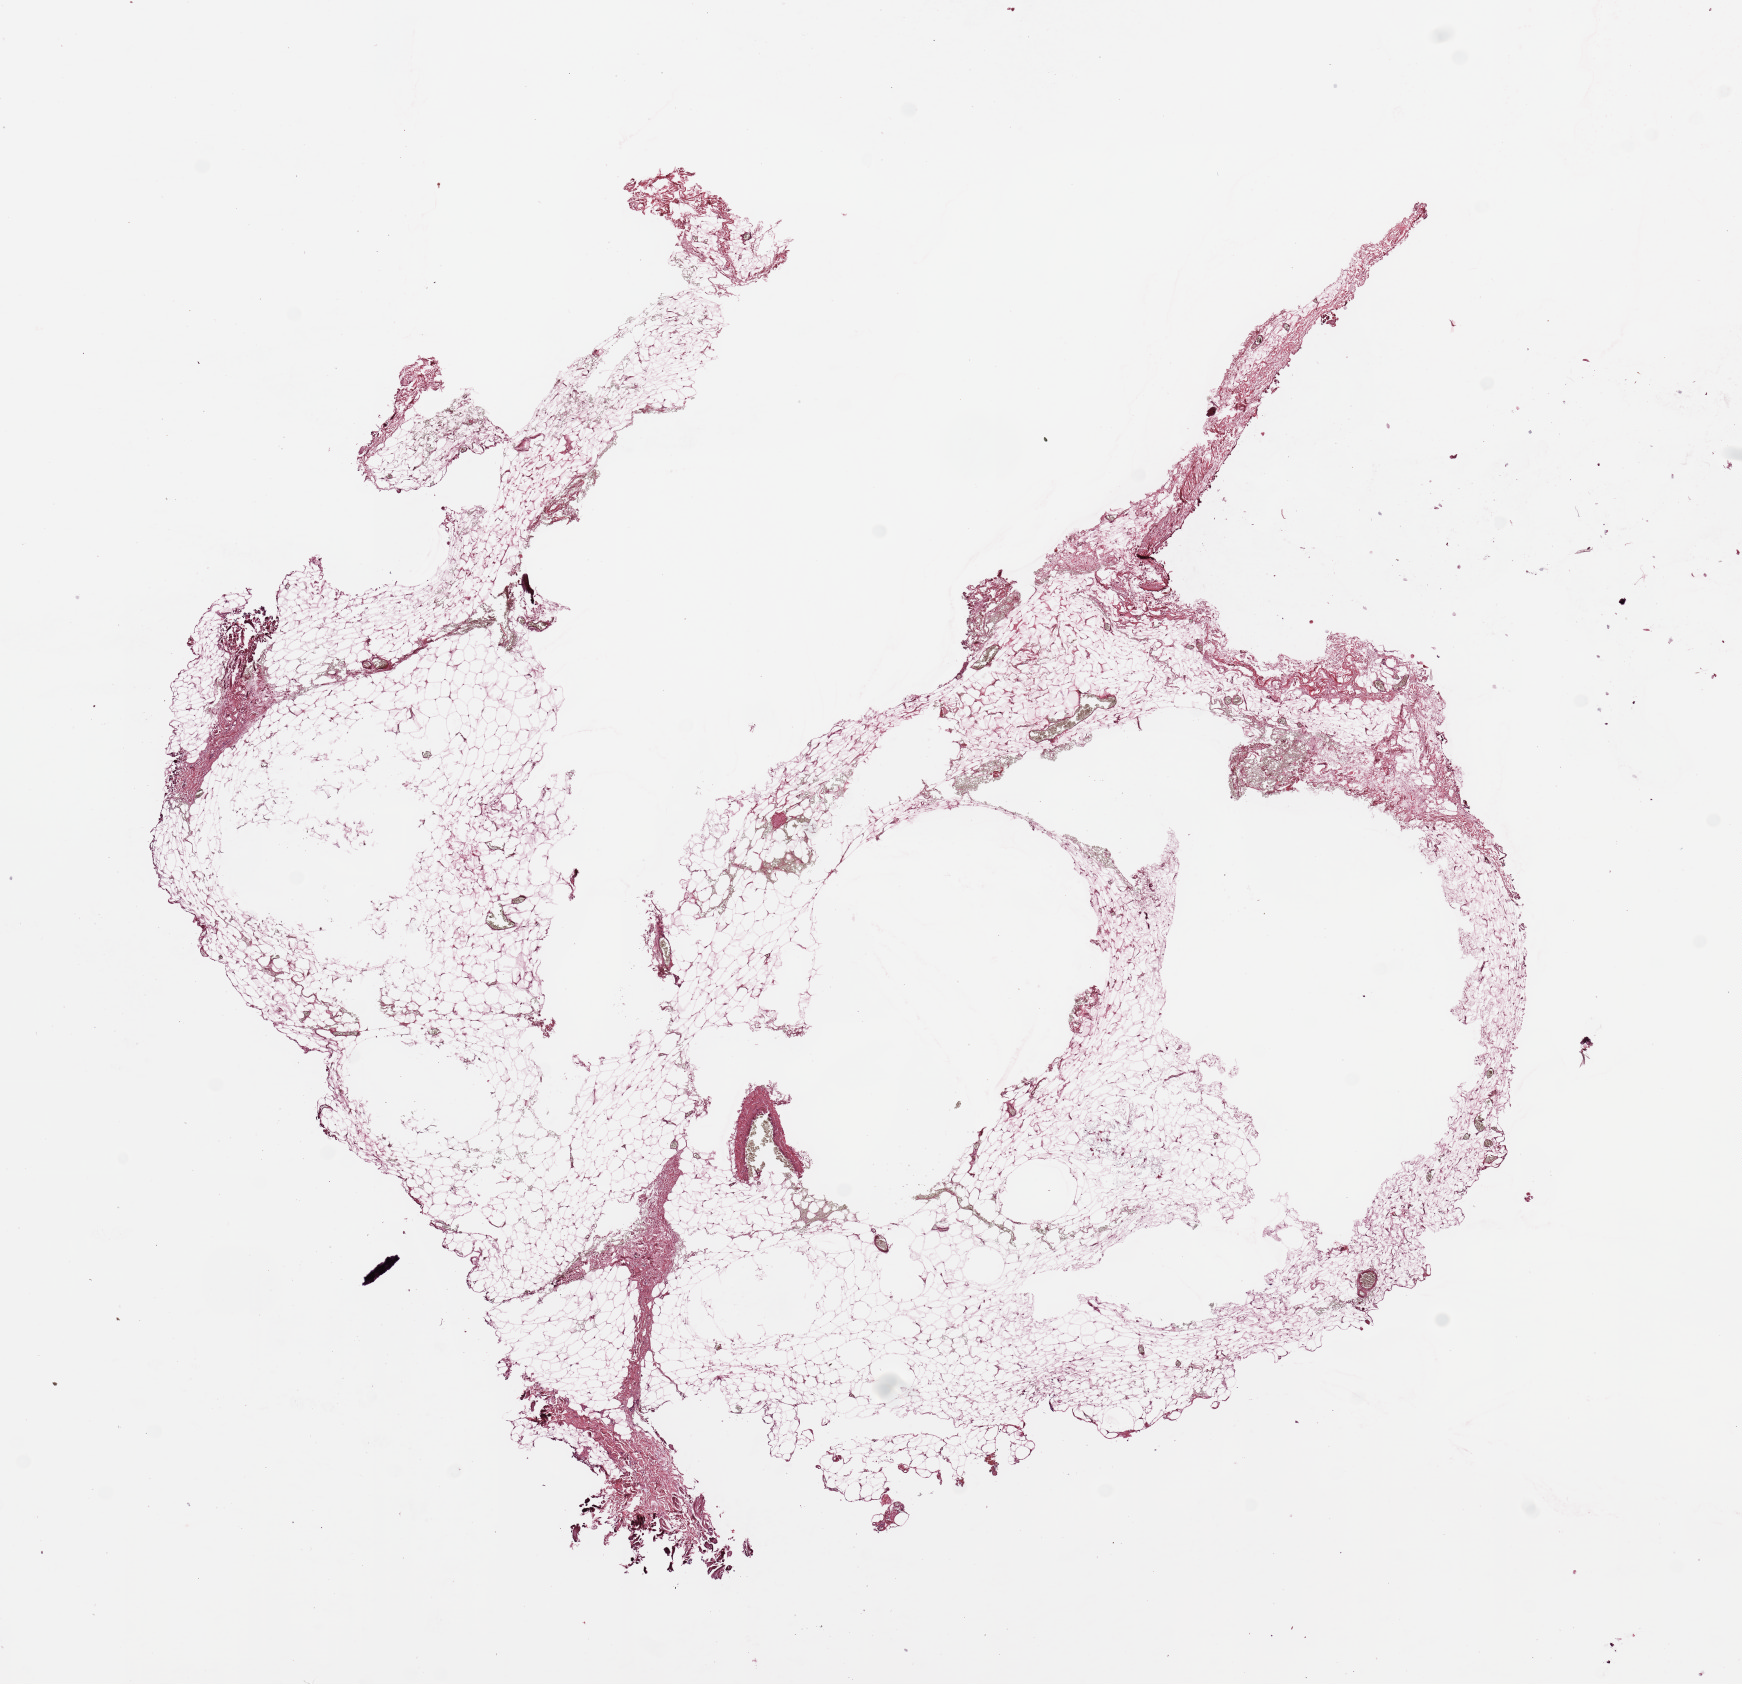
Whole-slide histology image, H&E, whole scanned area (about 13.8 x 13.3 mm, from a 20x scan) shown as a low-resolution overview, normal (non-tumour) tissue (melanoma cohort); sampled site not recorded. Male, 60 y/o.
This section: normal (non-tumour) tissue from the same patient. Patient diagnosis (cohort enrolment): cutaneous melanoma (skin).